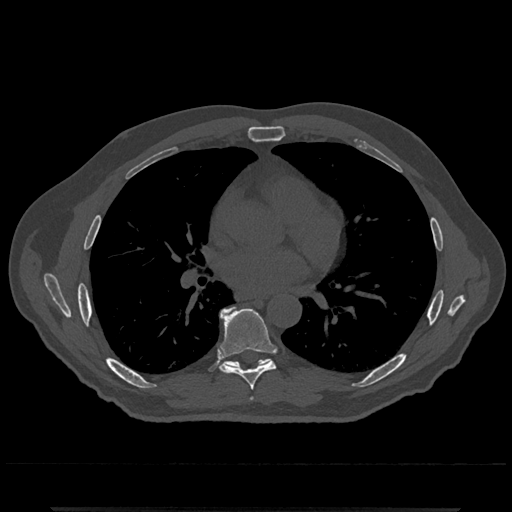
CT including the spine, one axial slice. Position 710 of 797 along the scan axis. Reconstruction kernel Br40s/3. Bone window (W 1800 / L 400 HU). 512 × 512 image matrix, field of view 393 × 393 mm. Patient: male, 67 years. Case-level facts recorded for this patient, not image findings: primary cancer: prostate.
Structures marked on this image (semi-automatically segmented with operator editing):
- T7 vertebra: box from (x=219, y=308) to (x=277, y=391) px
- T8 vertebra: (x=219, y=306)–(x=270, y=367)